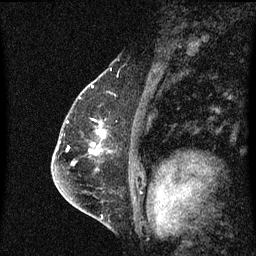
Breast MRI (dynamic contrast-enhanced), one sagittal slice; slice 43 of 60 in the series (ordered by position); dynamic contrast-enhanced series, image 2 of 3 at this slice position (ordered by acquisition); 1.5 T; TE 4.2 ms, TR 8.4 ms; 2 mm slice thickness; 256 × 256 image matrix, field of view 200 × 200 mm. Female patient, age 57 years. Case-level facts recorded for this patient, not image findings: setting: breast cancer imaged before/during neoadjuvant chemotherapy; receptor status: HR-positive, HER2-negative.
Structures marked on this image (semi-automatically segmented with operator editing):
- analysis volume of interest (the breast-tissue region the enhancement analysis was run in; not a lesion): bounding box [x1, y1, x2, y2] px = [92, 124, 107, 145]
- tumour enhancement mask (voxels above the 70 % enhancement threshold inside the analysis volume of interest): [101, 130, 106, 139]